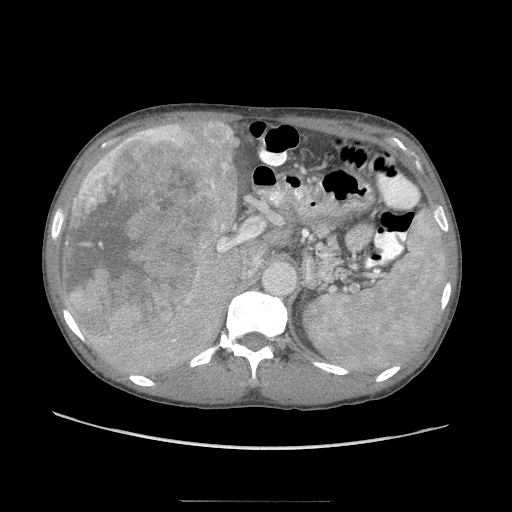
Contrast-enhanced abdominal CT (liver protocol), one axial slice; reconstruction kernel STANDARD; soft-tissue window (W 400 / L 40 HU); 2.5 mm slice thickness; 512 × 512 image matrix, field of view 380 × 380 mm. From the clinical record (not read from this slice): diagnosis: hepatocellular carcinoma (patient treated with transarterial chemoembolisation; whether this scan precedes or follows treatment is not stated here); TNM stage (as recorded): Stage-IIIA; Child-Pugh class: A.
Structures marked on this image (semi-automatic segmentation, software-assisted and operator-edited):
- liver parenchyma outside the tumour (the mass and vessels are separate outlines, so this box may not span the whole liver): bounding box (x1, y1, x2, y2) in pixels: (60, 120, 260, 376)
- mass: (61, 121, 241, 344)
- liver vessels: (213, 188, 221, 256)